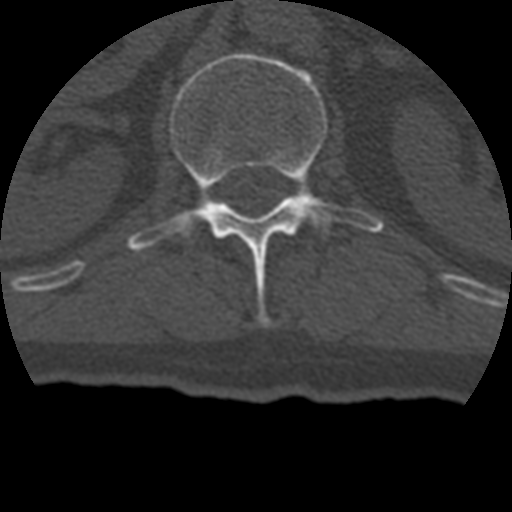
CT including the spine, one axial slice. Position 143 of 399 along the scan axis. 120 kVp. Bone window (W 1800 / L 400 HU). 512 × 512 image matrix, field of view 160 × 160 mm. Patient age 69 years. From the clinical record (not read from this slice): primary cancer: prostate.
Annotated regions visible in this slice (semi-automatically segmented with operator editing):
- L1 vertebra: bounding box (x1, y1, x2, y2) in pixels: (127, 53, 384, 326)